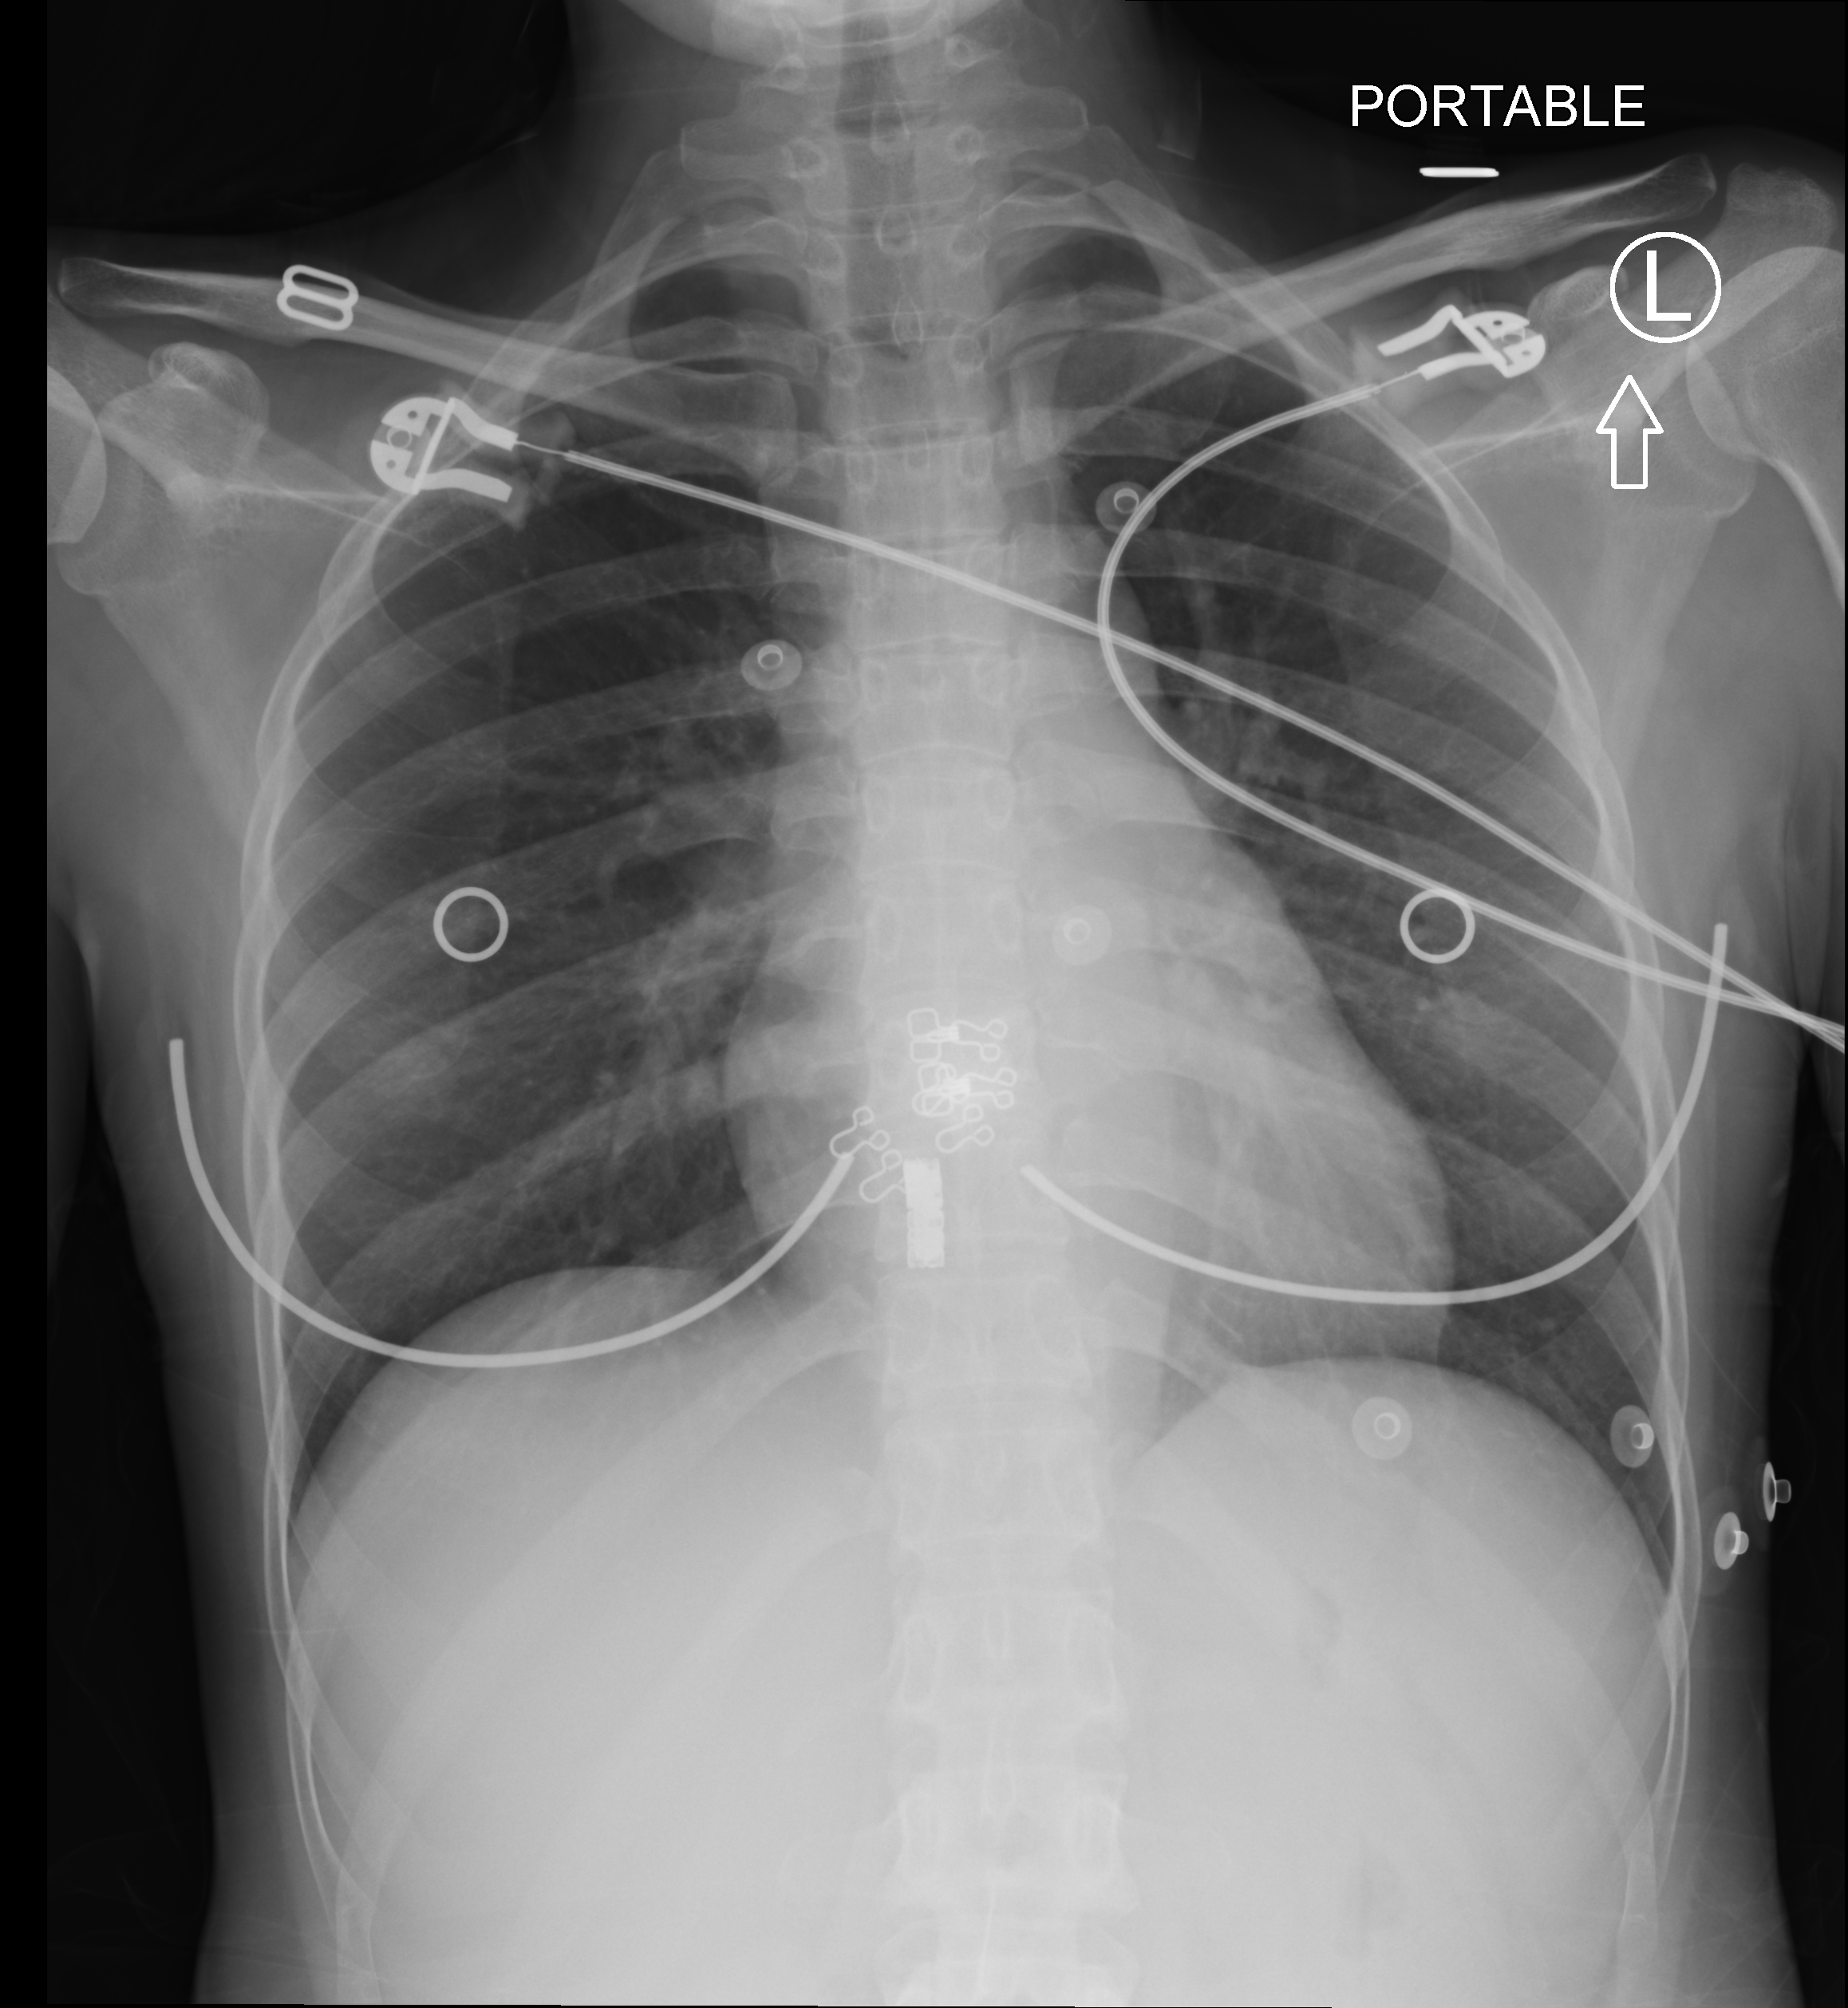
Bedside chest radiograph (computed radiography), anteroposterior (AP) projection. Female patient hospitalised with COVID-19, age 18–59 years.
Admission-level facts for this patient (not findings on this image; timing relative to this image not recorded):
- mechanically ventilated during this hospital stay: no
- length of hospital stay: 18 days